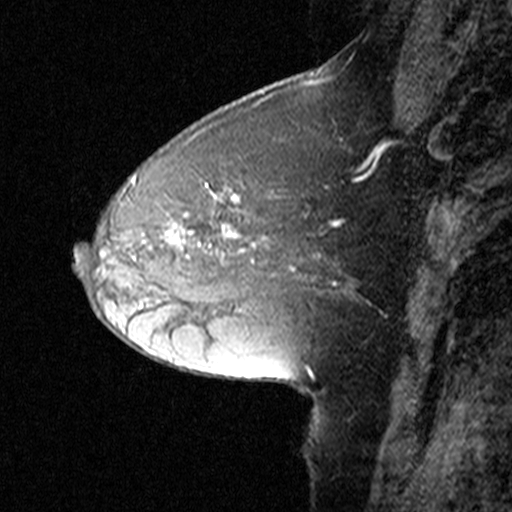
Breast MRI (dynamic contrast-enhanced), one sagittal slice; position 18 of 44 along the scan axis; dynamic contrast-enhanced study with each time point stored as its own series, time point 2 of 3 at this slice position (early post-contrast, ordered by acquisition time); 1.5 T; TE 4.5 ms, TR 11 ms; 3 mm slice thickness; 512 × 512 image matrix. Female patient, age 50 years. Case-level facts recorded for this patient, not image findings: setting: breast cancer imaged before/during neoadjuvant chemotherapy; receptor status: HR-positive, HER2-negative.
Structures marked on this image (semi-automatically segmented with operator editing):
- analysis volume of interest (the breast-tissue region the enhancement analysis was run in; not a lesion): box from (x=126, y=162) to (x=314, y=291) px
- tumour enhancement mask (voxels above the 90 % enhancement threshold inside the analysis volume of interest): (x=133, y=172)–(x=309, y=246)